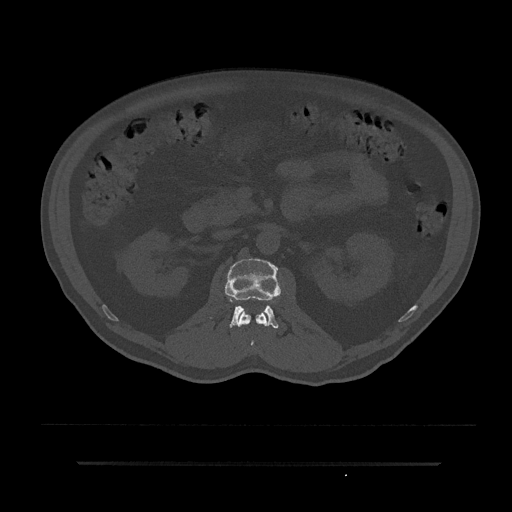
CT including the spine, one axial slice. Position 105 of 797 along the scan axis. Reconstruction kernel Br40s/3. 120 kVp. Bone window (W 1800 / L 400 HU). 0.5 mm slice thickness. 512 × 512 image matrix, field of view 464 × 464 mm. Male patient, age 59 years. From the clinical record (not read from this slice): primary cancer: bile ducts; vertebrae with lytic lesions (as recorded): T10.
Annotated regions visible in this slice (semi-automatically segmented with operator editing):
- L1 vertebra: bounding box <238,310,268,347> (left, top, right, bottom; pixels)
- L2 vertebra: <225,258,281,329>